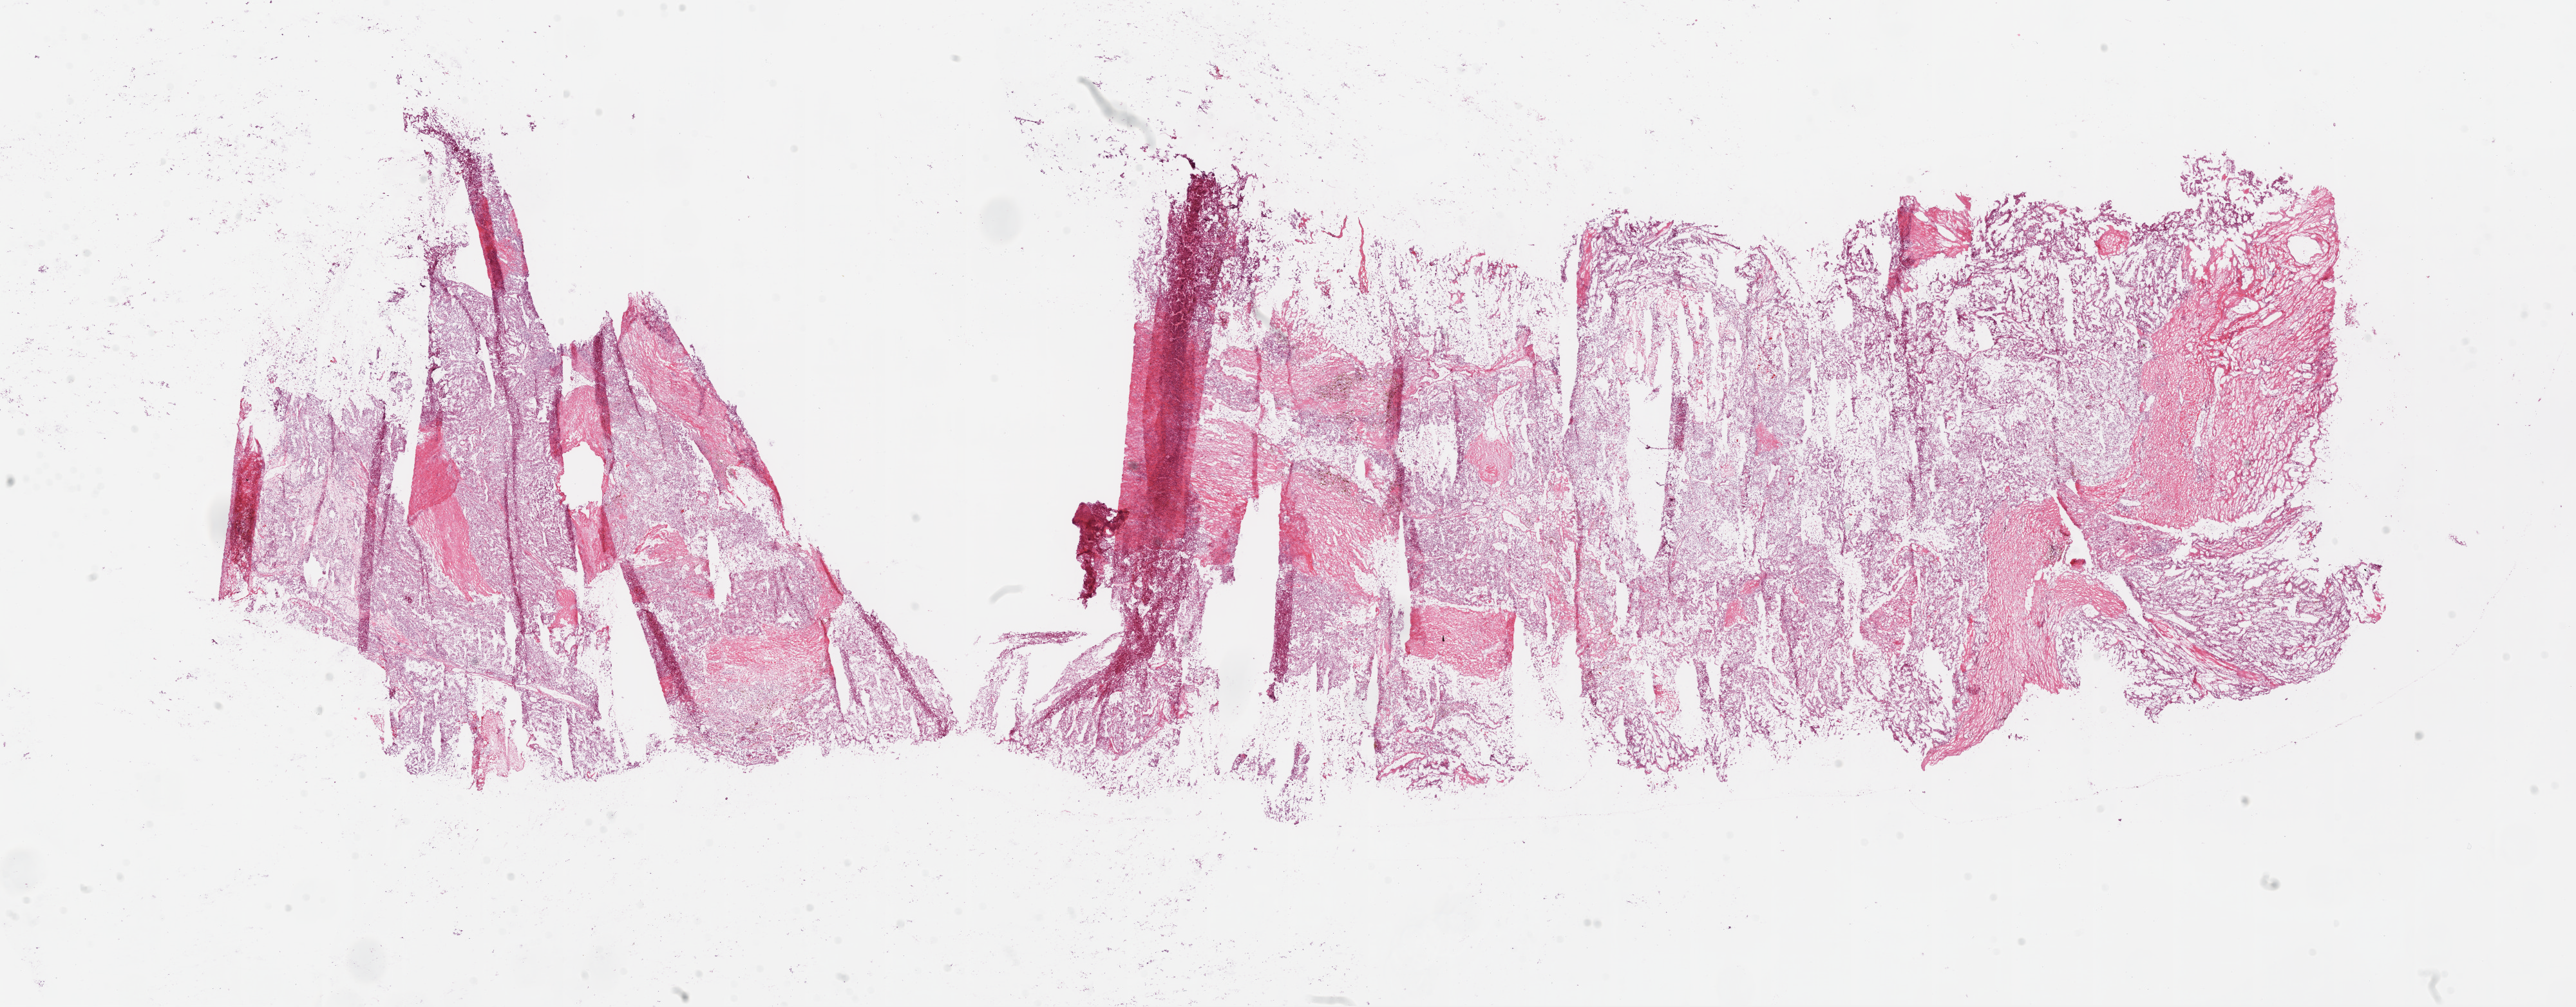
Hematoxylin and eosin (H&E) stained whole-slide image, shown as a low-resolution overview of the whole scanned area (about 32.1 x 12.5 mm, slide scanned at 20x). Frozen section from the bottom of the tissue portion. Kidney, primary tumour sample. Male, age 51 years at initial diagnosis. Histologic grade: G3 (poorly differentiated). Composition of this section per pathologist review: tumour cells 80%, tumour nuclei 80%, normal cells 0%, stromal cells 20%, necrosis 0%.
• AJCC pathologic stage: III
• diagnosis: Clear cell adenocarcinoma, NOS
• laterality: right
• TNM: T3a N0 M0